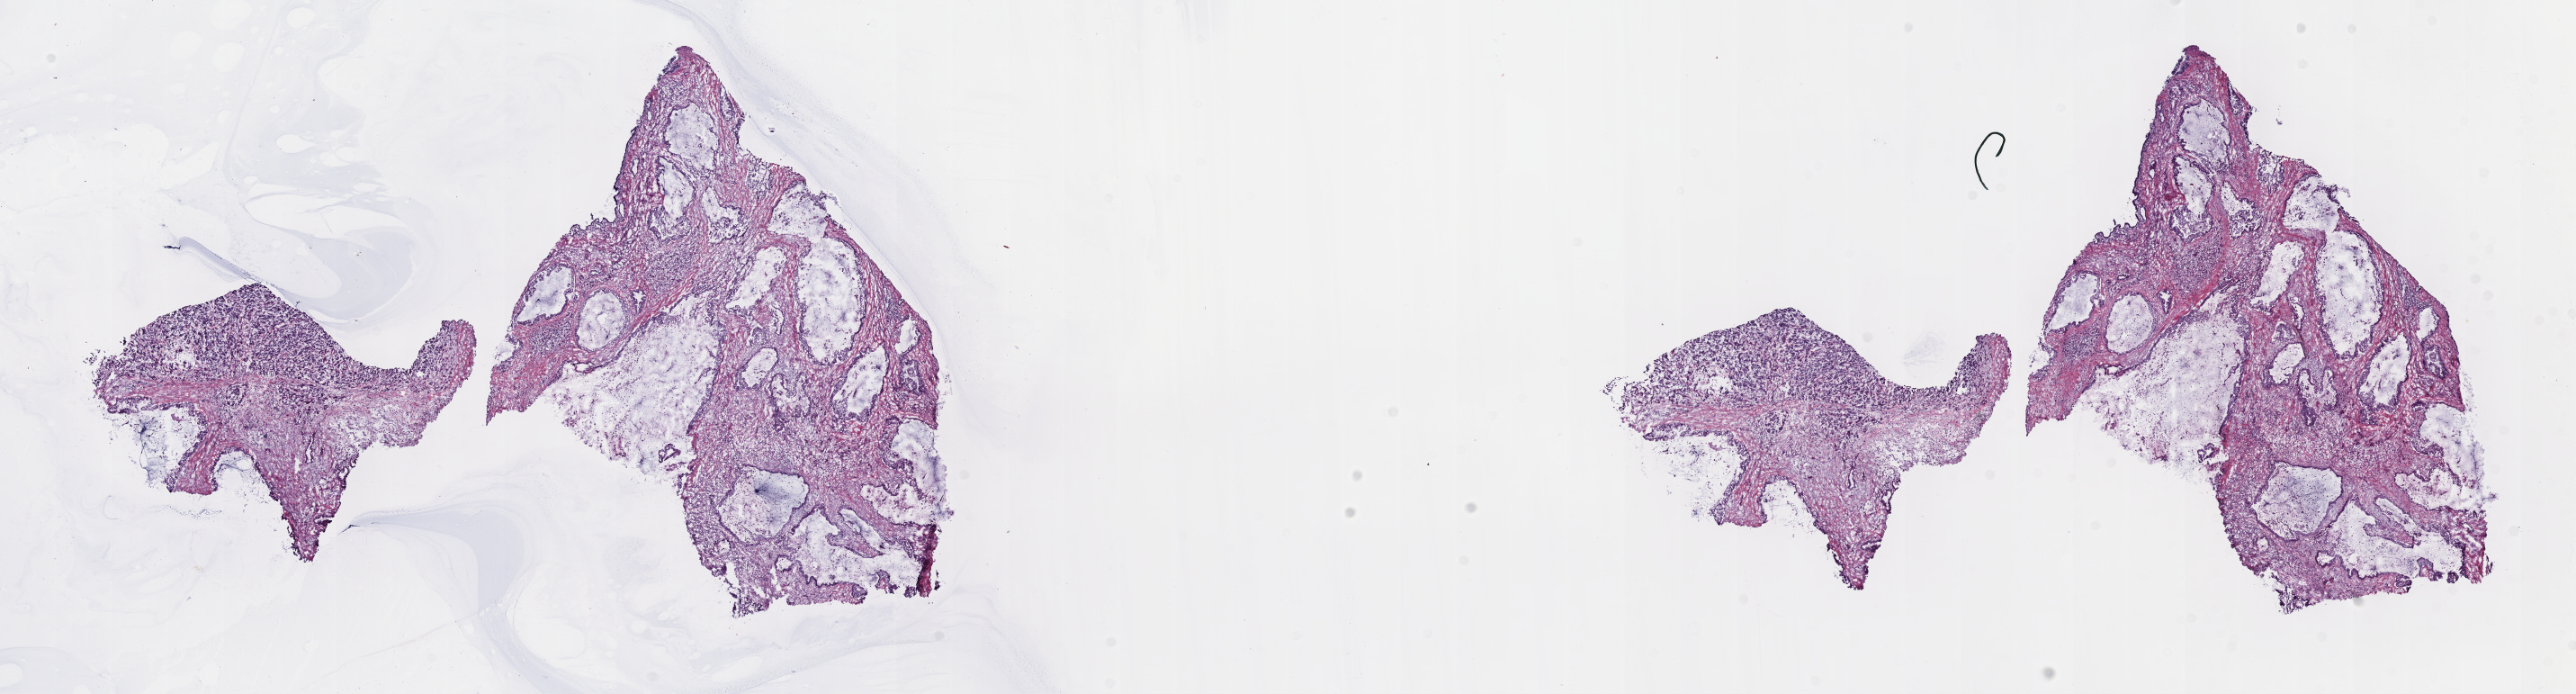
Whole-slide histology image, H&E-stained, a low-resolution overview of the entire scanned area, about 23.2 x 6.2 mm (from a 40x scan), frozen section from the top of the tissue portion, primary tumour sample from the pancreas. Male, age 76 years at initial diagnosis.
Histologic diagnosis: Infiltrating duct carcinoma, NOS.